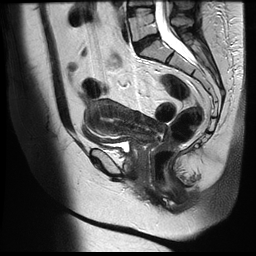
Pelvic MRI for cervical cancer, one sagittal slice; position 16 of 35 along the scan axis; T2-weighted; 1.5 T; TE 122.8 ms, TR 4992 ms; 4 mm slice thickness; 256 × 256 image matrix, field of view 300 × 300 mm. Patient: female, 42 years.
Annotated regions visible in this slice (expert manual segmentation):
- uterus and cervix: bounding box [x1, y1, x2, y2] px = [83, 98, 166, 149]